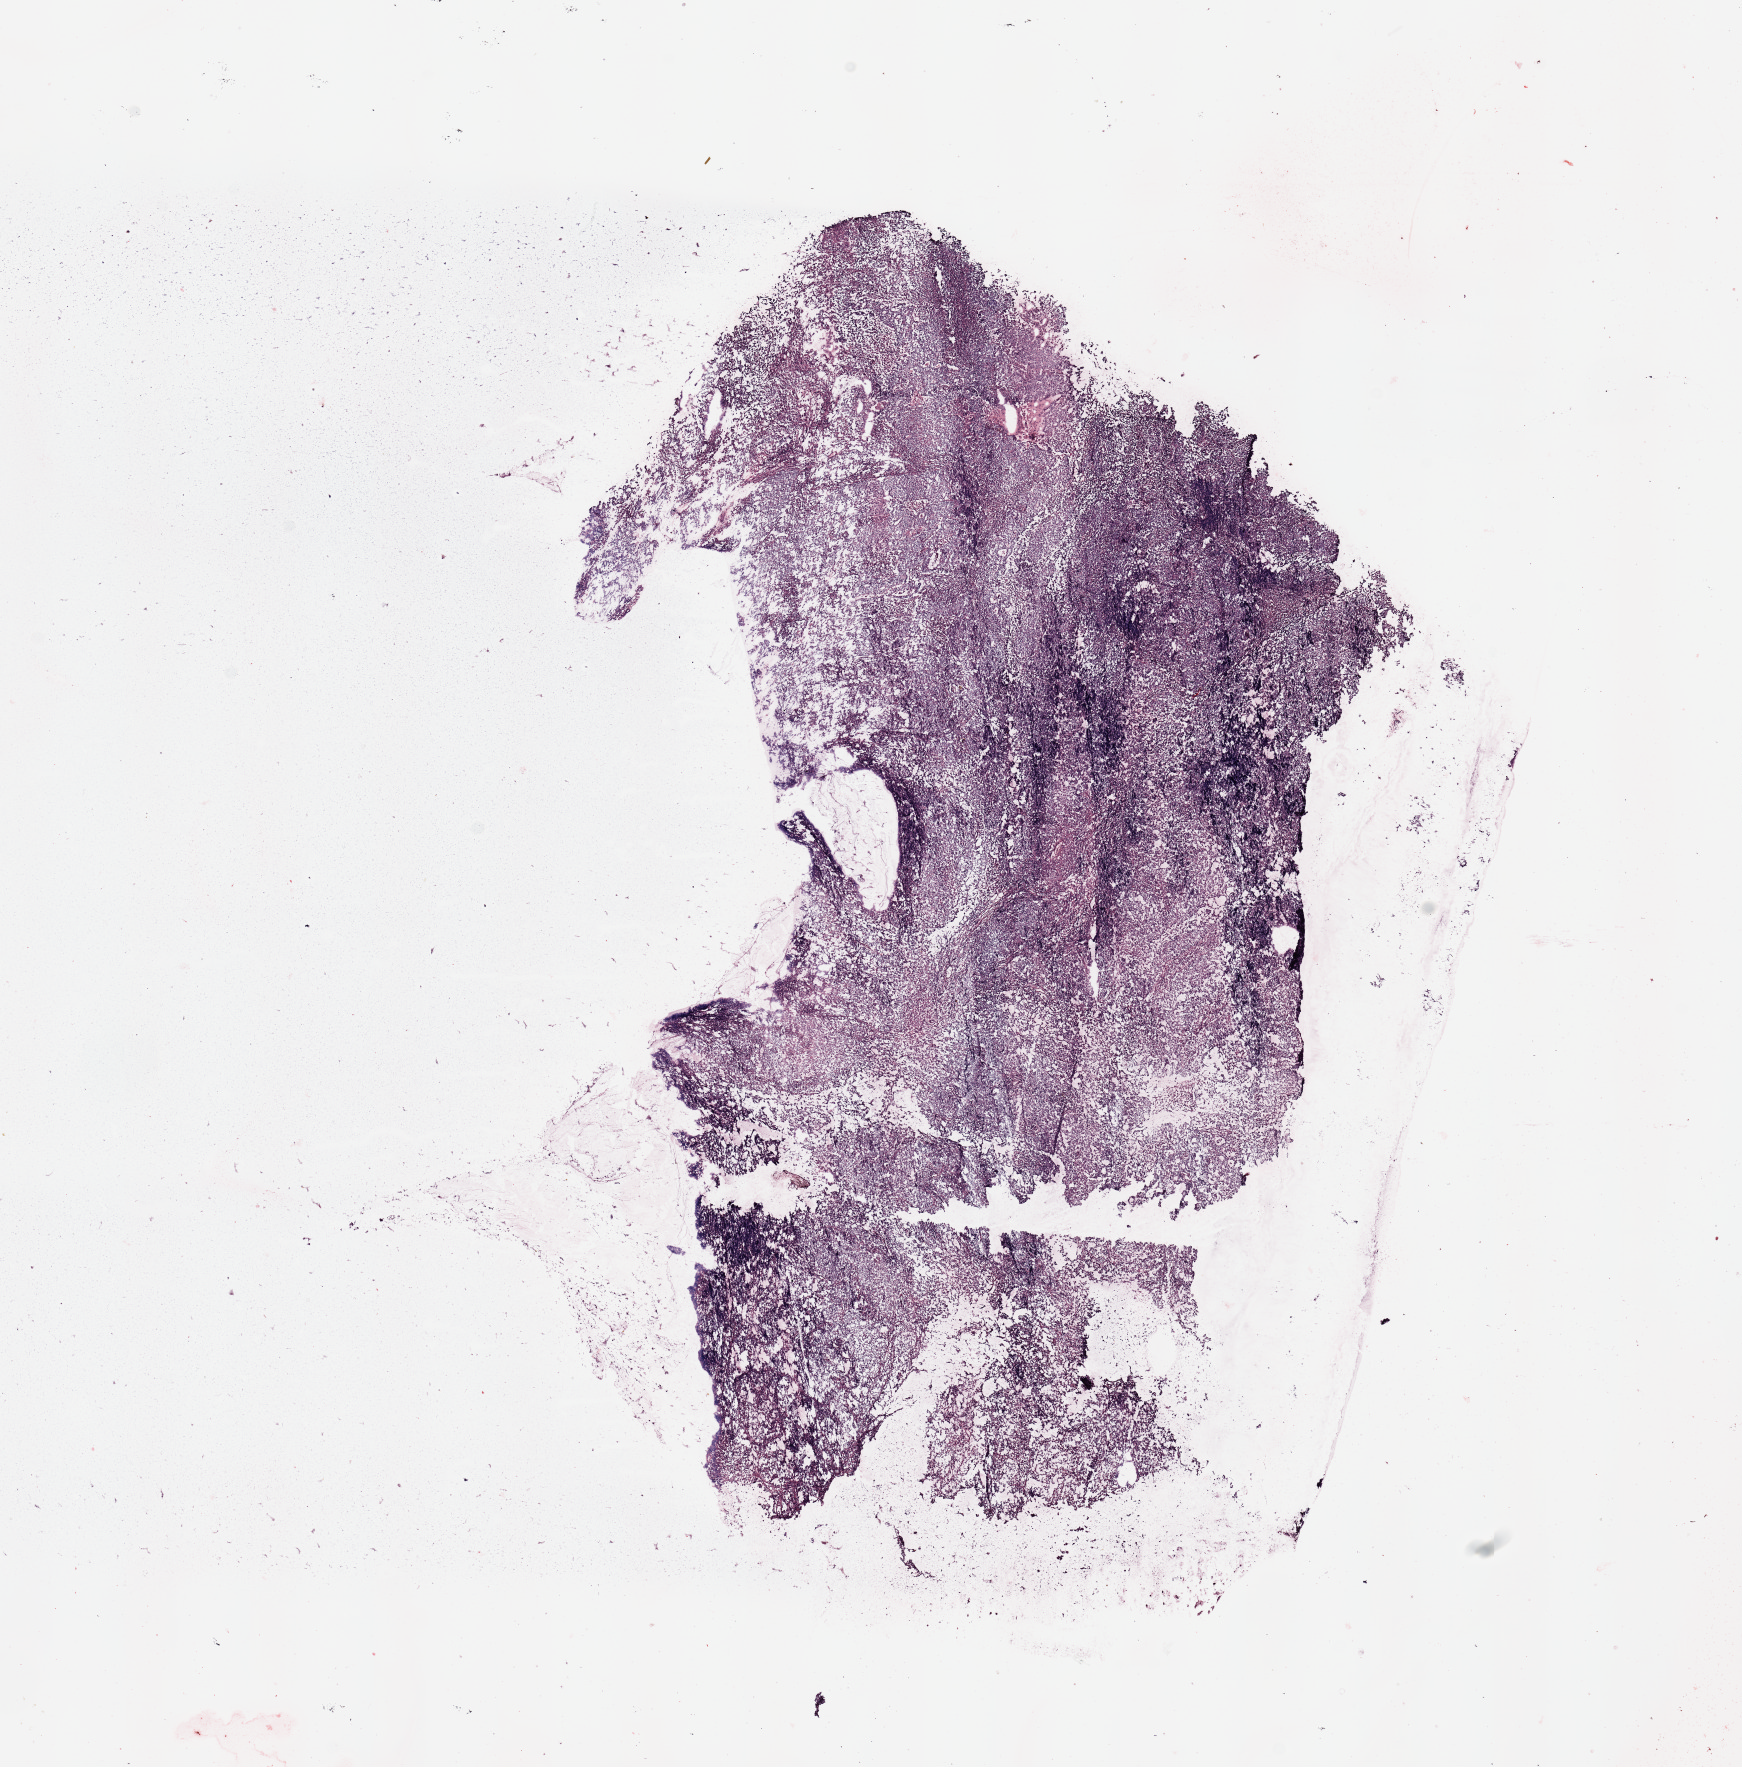
H&E-stained whole-slide image, shown as a low-resolution overview of the whole scanned area (about 13.8 x 14.0 mm, slide scanned at 20x); tumour tissue sample, sampled site: uterus. Patient: female, age 62 years. Histologic grade: G3 (poorly differentiated). Slide review estimates, as recorded: tumour nuclei 85%, necrosis 0%.
AJCC pathologic stage: I. Histologic diagnosis: Endometrioid adenocarcinoma, NOS.